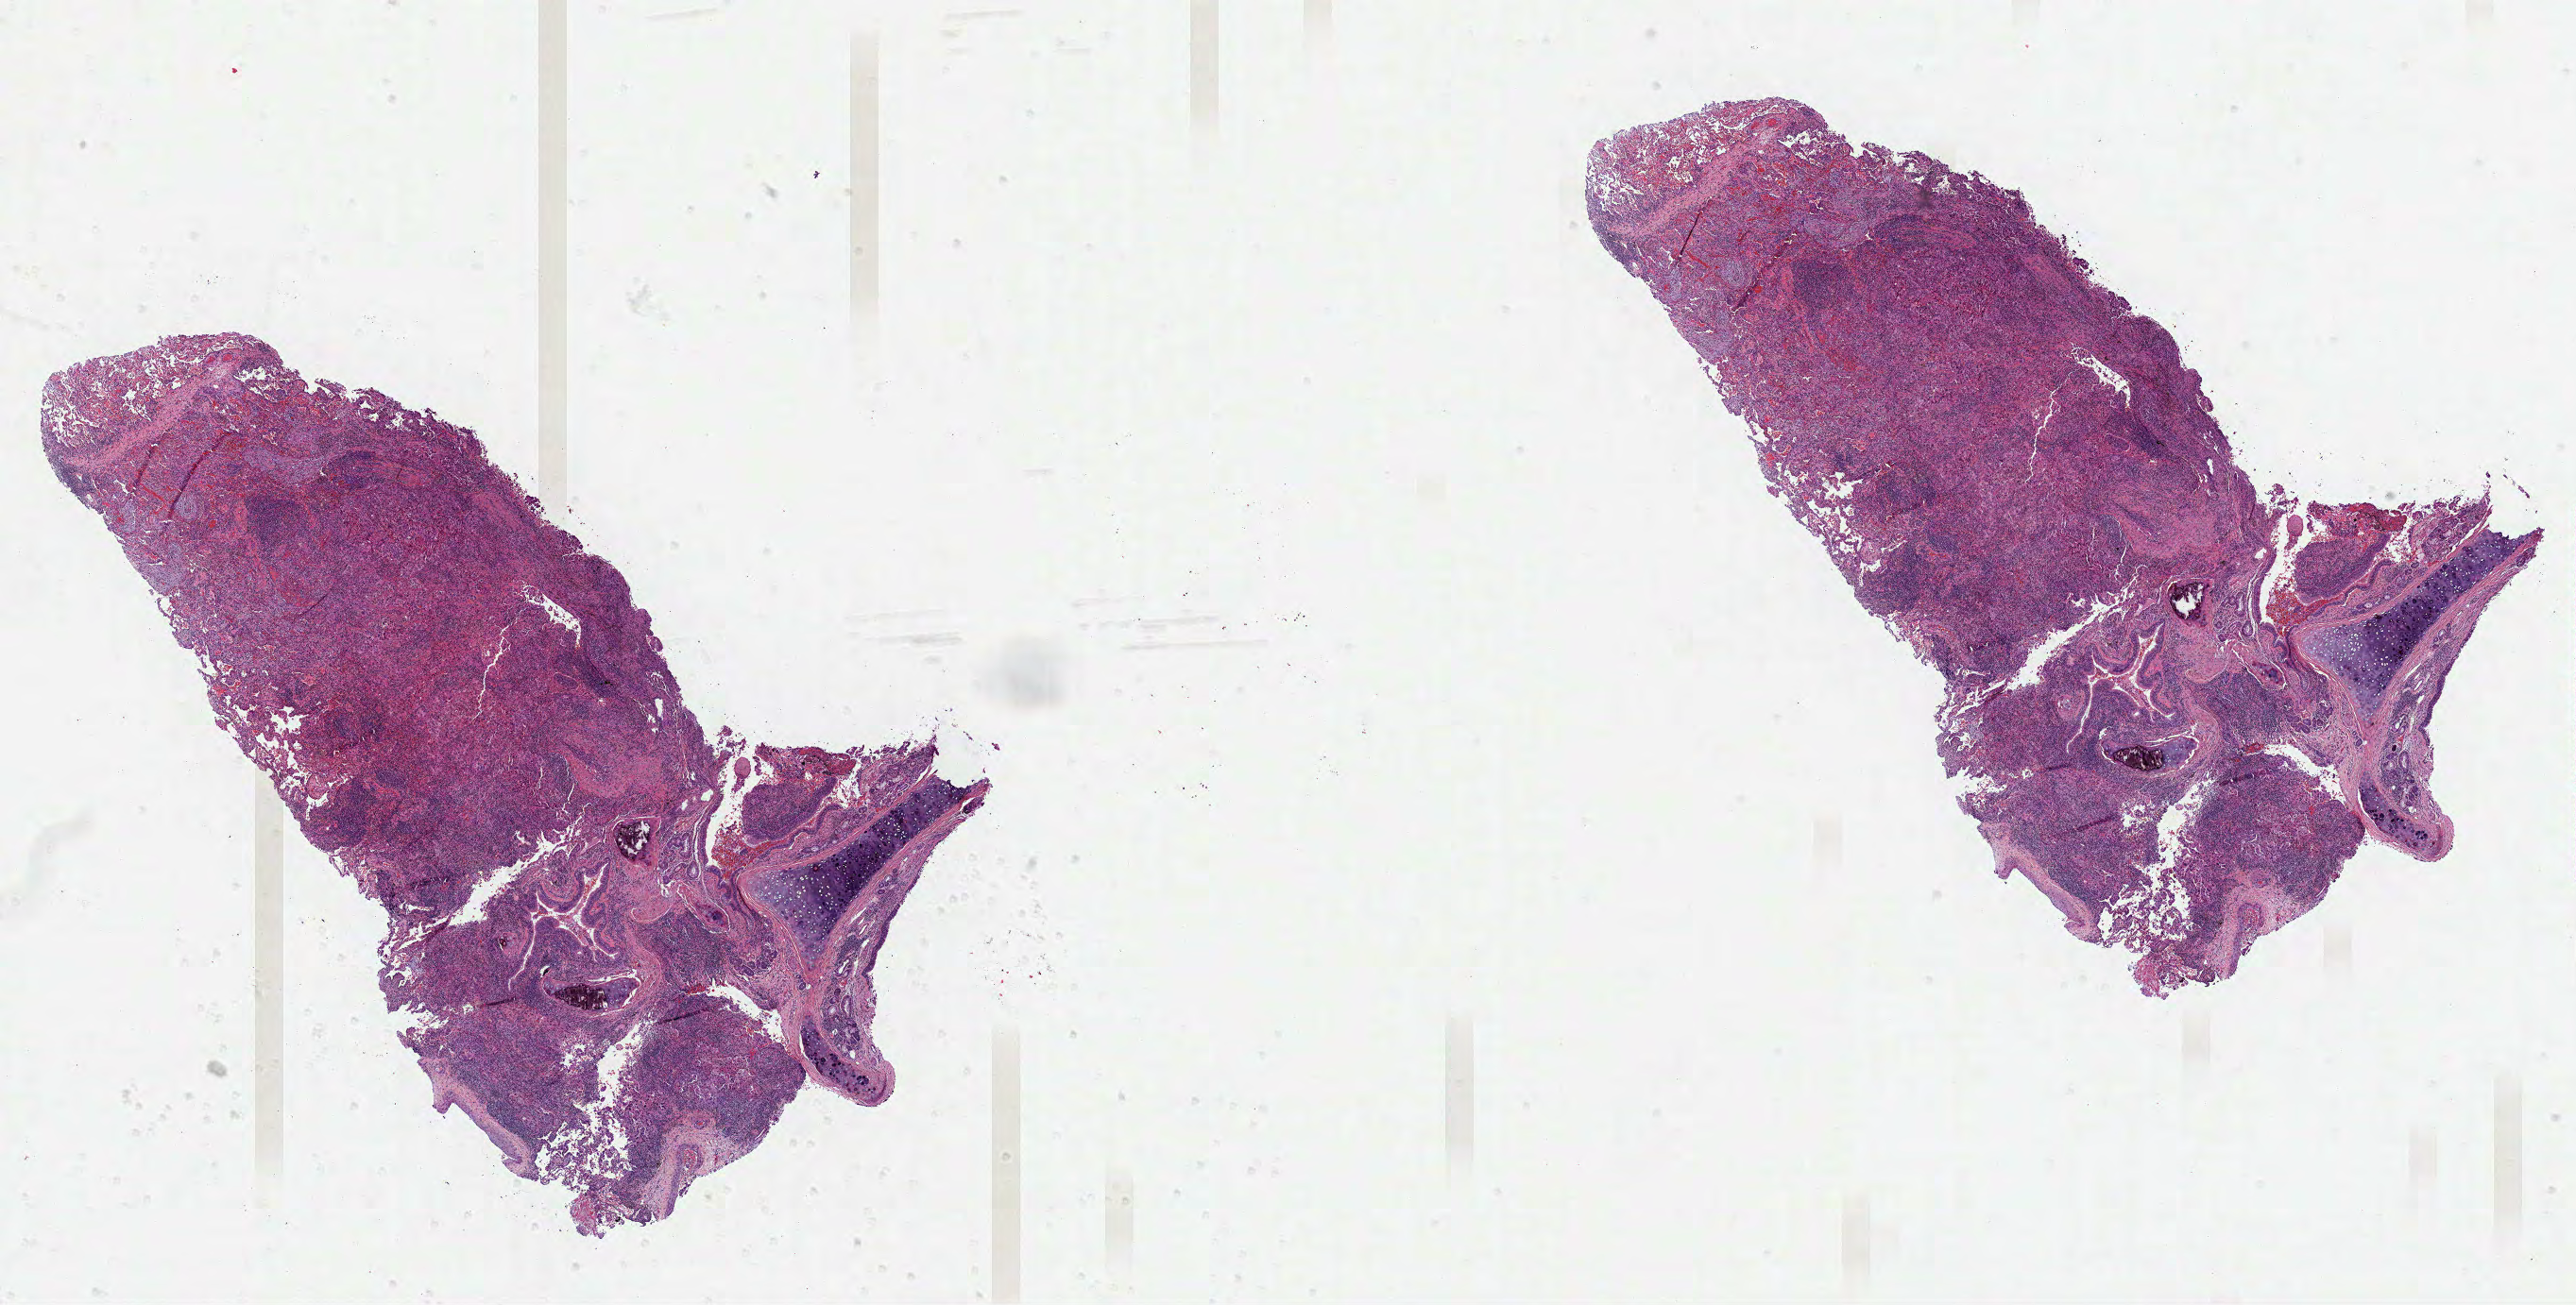
Whole-slide histology image, H&E — shown as a low-resolution overview of the whole scanned area (about 22.0 x 11.1 mm); FFPE section; lung, primary tumour sample. Female, age 52 years at initial diagnosis.
Laterality: left. AJCC pathologic stage: IA (7th edition). Pathologic diagnosis: Adenocarcinoma, NOS. TNM: T1b N0 M0.